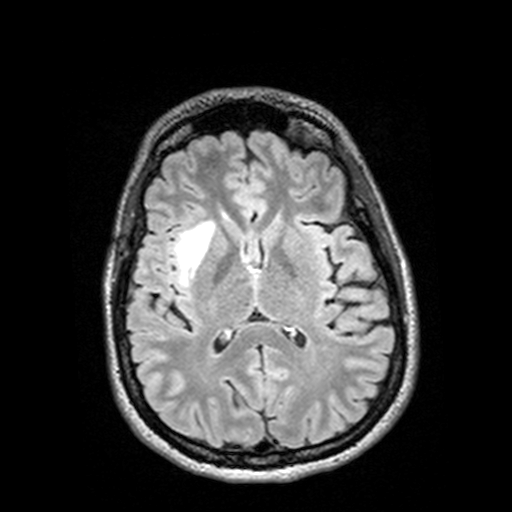
Brain MRI from a brain-tumour surgery series, one axial slice; position 65 of 144 along the scan axis; T2 FLAIR; 512 × 512 image matrix. From the clinical record (not read from this slice): histopathology: Astrocytoma; WHO grade: 3; IDH mutation: yes.
Outlined on this slice (manually delineated by an expert):
- tumour: box from (x=192, y=224) to (x=230, y=286) px